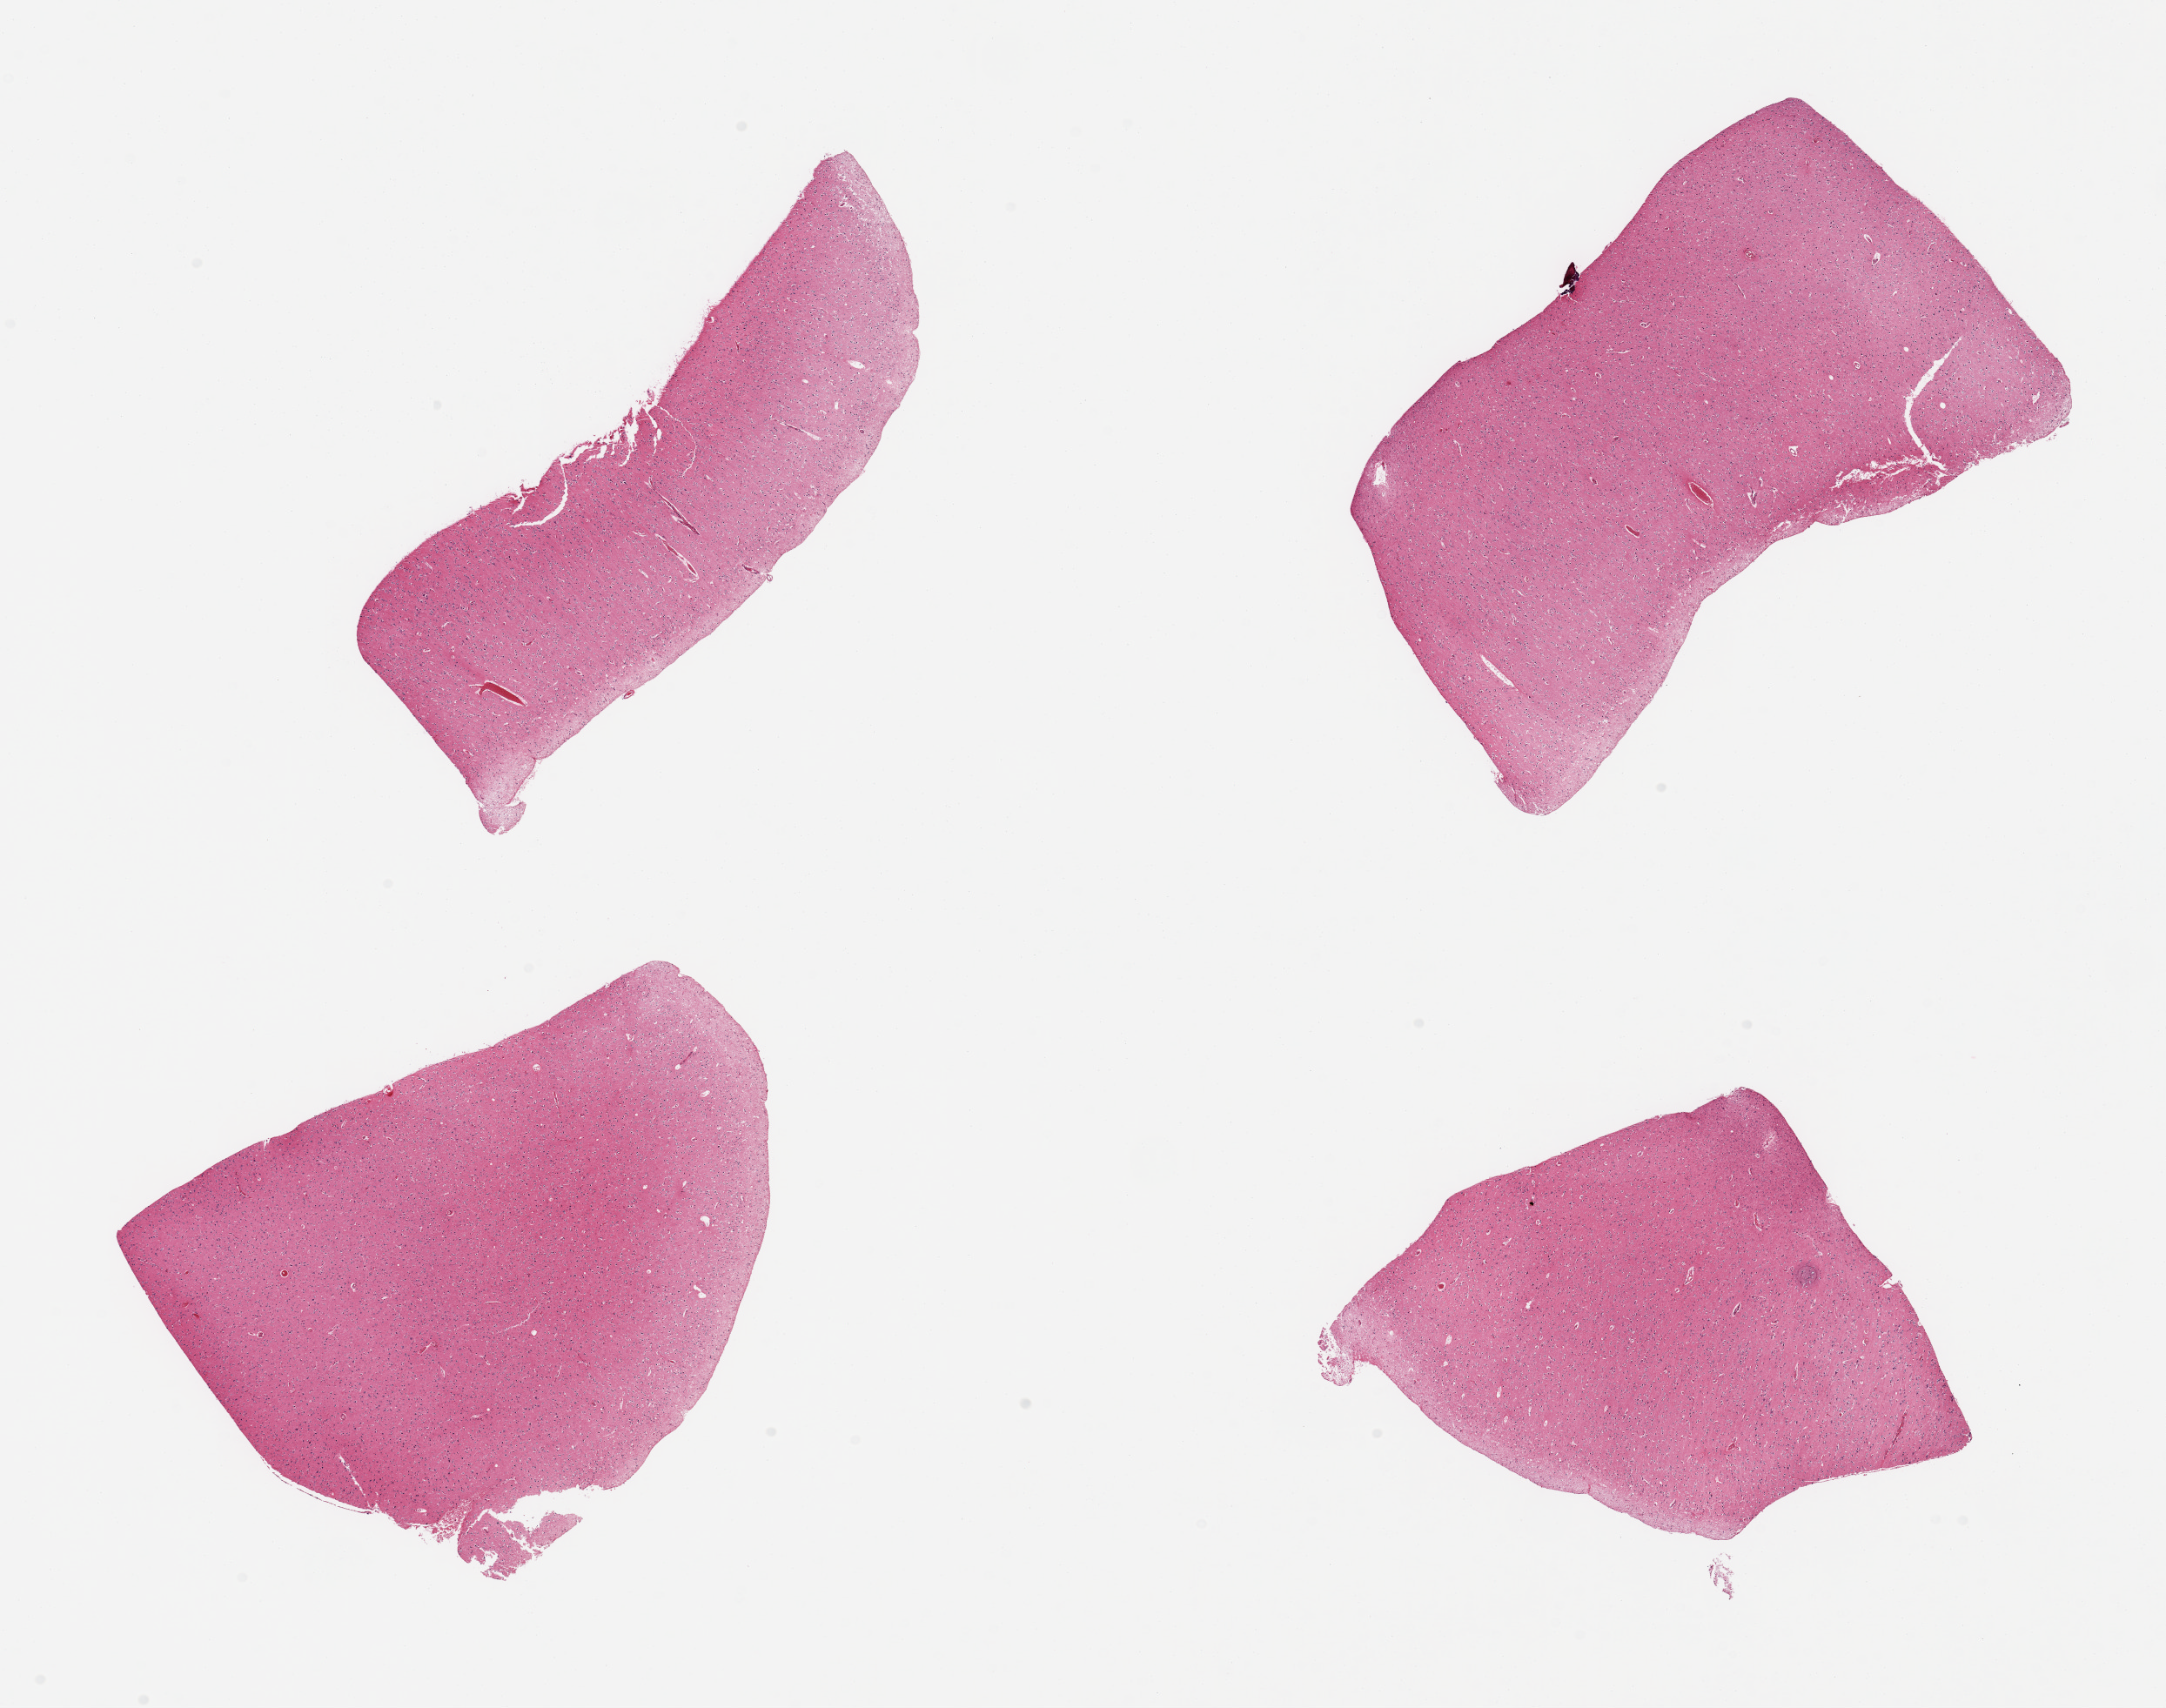
Digitized haematoxylin and eosin-stained section, shown as a low-resolution overview of the whole scanned area (about 19.7 x 15.5 mm, acquisition: 20x scan). PAXgene-fixed paraffin-embedded (PFPE) section. Sampled site (target tissue): cerebral cortex. Tissue donor sample. Male donor.
Pathologist's review note for this sample: 4 pieces, no abnormalities.